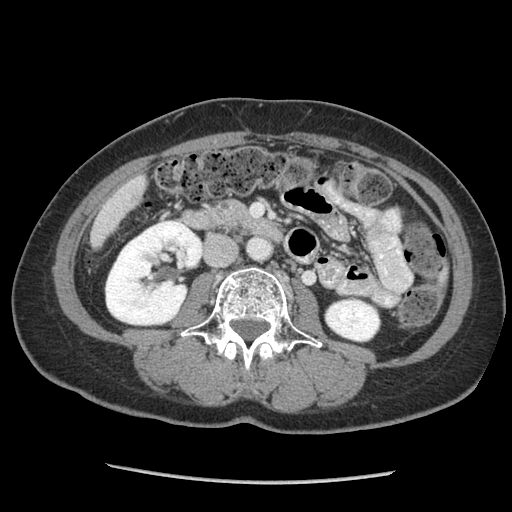
Contrast-enhanced abdominal CT (liver protocol), one axial slice; slice 17 of 105 in the series (ordered by position); reconstruction kernel STANDARD; 140 kVp; soft-tissue window (W 400 / L 40 HU); 2.5 mm slice thickness; 512 × 512 image matrix. Case-level facts recorded for this patient, not image findings: diagnosis: hepatocellular carcinoma (patient treated with transarterial chemoembolisation; whether this scan precedes or follows treatment is not stated here); TNM stage (as recorded): Stage-I; Child-Pugh class: A.
Annotated regions visible in this slice (semi-automatic segmentation, software-assisted and operator-edited):
- liver parenchyma outside the tumour (the mass and vessels are separate outlines, so this box may not span the whole liver): bounding box (x1, y1, x2, y2) in pixels: (90, 174, 146, 247)